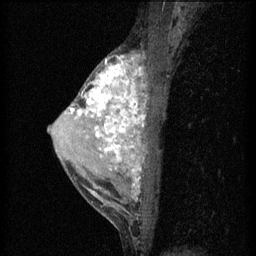
Breast MRI (dynamic contrast-enhanced), one sagittal slice; slice 36 of 60 in the series (ordered by position); 3 images stored at this slice position (order not interpretable as contrast timing); 1.5 T; TE 4.2 ms, TR 11 ms; 2 mm slice thickness; 256 × 256 image matrix. Patient: female, 40 years.
Structures marked on this image (semi-automatic segmentation, software-assisted and operator-edited):
- analysis volume of interest (the breast-tissue region the enhancement analysis was run in; not a lesion): bounding box (x1, y1, x2, y2) in pixels: (55, 52, 157, 203)
- tumour enhancement mask (voxels above the 70 % enhancement threshold inside the analysis volume of interest): (71, 56, 146, 201)